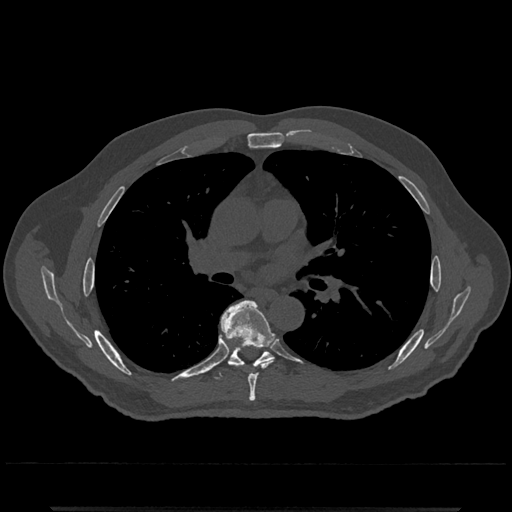
CT including the spine, one axial slice. Bone window (W 1800 / L 400 HU). 512 × 512 image matrix, field of view 393 × 393 mm. Male patient, age 67 years. From the clinical record (not read from this slice): primary cancer: prostate.
Structures marked on this image (semi-automatic segmentation, software-assisted and operator-edited):
- T6 vertebra: bounding box <221,300,275,402> (left, top, right, bottom; pixels)
- T7 vertebra: <213,334,273,379>